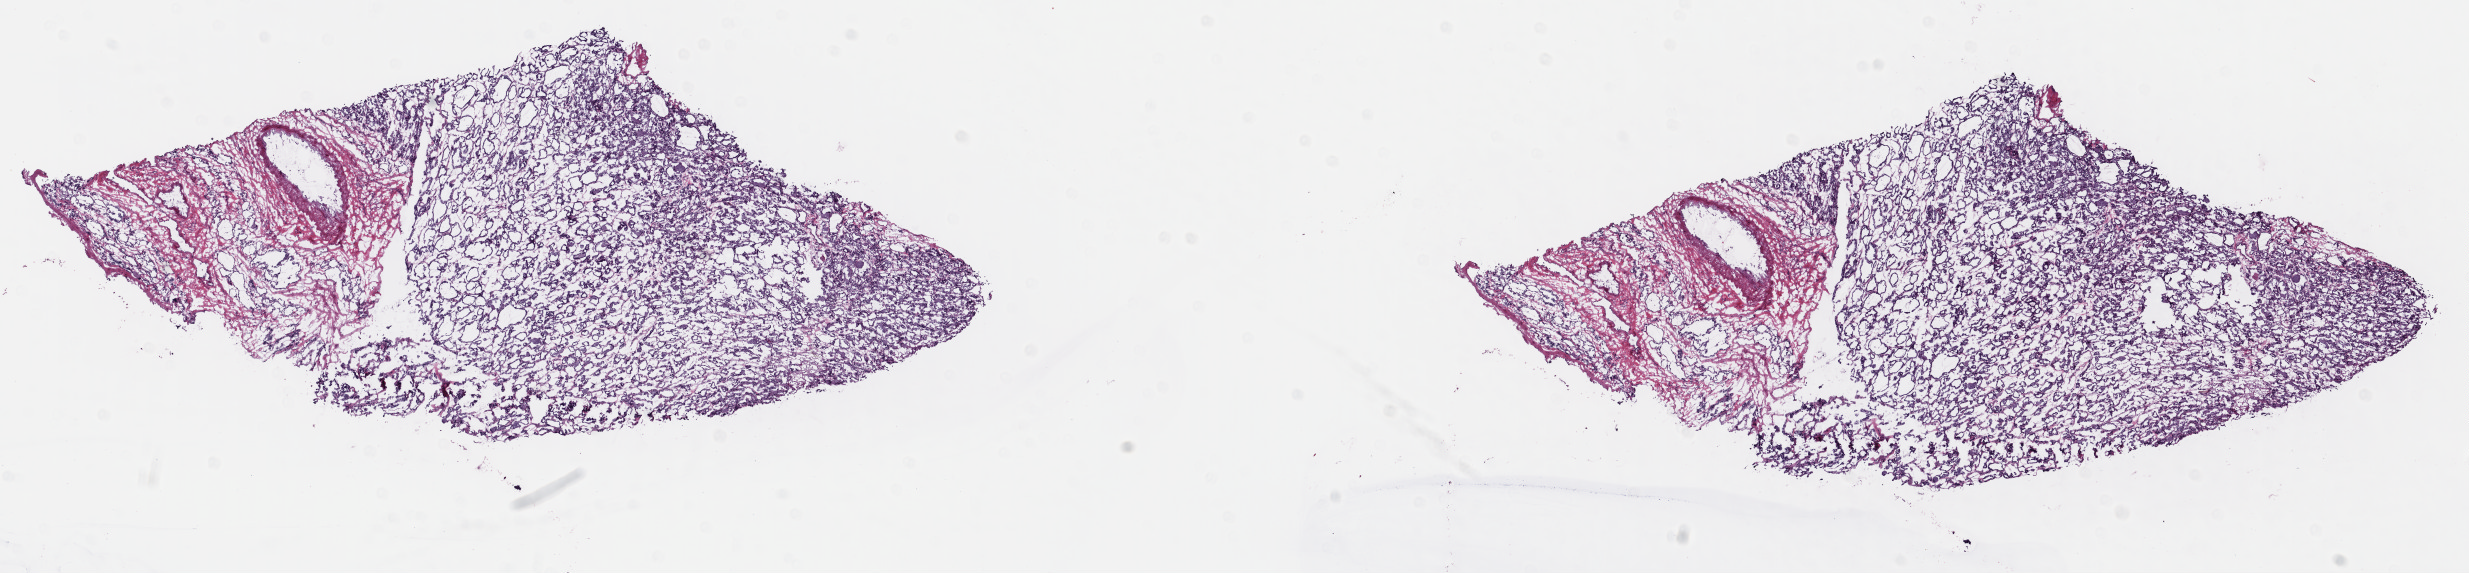
Digitized H&E tissue section (whole slide), whole scanned area (about 19.4 x 4.5 mm, from a 40x scan) shown as a low-resolution overview, frozen section from the top of the tissue portion, sample: primary tumour, thyroid. Patient: female, age at initial diagnosis 53 years. Slide review estimates, as recorded: tumour cells 75%, tumour nuclei 85%, normal cells 20%, stromal cells 5%, necrosis 0%. Infiltration values recorded for this section: lymphocyte infiltration 0%, monocyte infiltration 1%, neutrophil infiltration 0%.
• pathologic diagnosis: Papillary carcinoma, follicular variant (thyroid gland)
• AJCC pathologic stage: II
• lymph nodes positive (case pathology): 0 of 5 examined